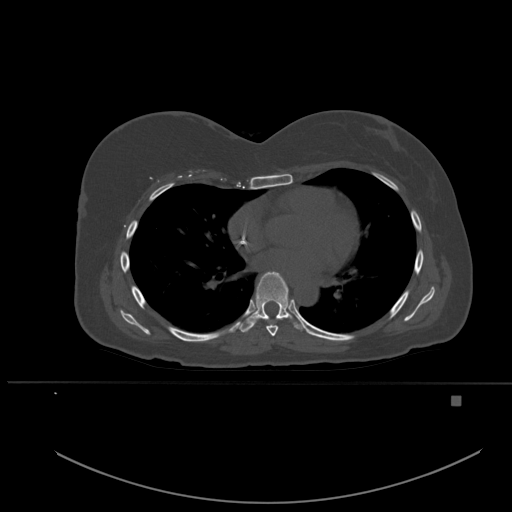
CT including the spine, one axial slice. Bone window (W 1800 / L 400 HU). 1.5 mm slice thickness. 512 × 512 image matrix, field of view 443 × 443 mm. Patient: female, 49 years. From the clinical record (not read from this slice): primary cancer: breast.
Outlined on this slice (semi-automatic segmentation, software-assisted and operator-edited):
- T6 vertebra: bounding box (x1, y1, x2, y2) in pixels: (266, 324, 278, 337)
- T7 vertebra: (239, 272, 303, 333)